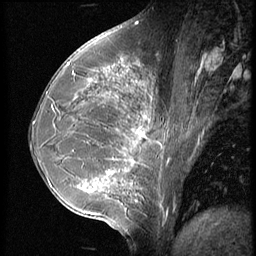
Breast MRI (dynamic contrast-enhanced), one sagittal slice. Position 26 of 56 along the scan axis. 3 images stored at this slice position (order not interpretable as contrast timing). 1.5 T. TE 4.2 ms, TR 9 ms. 2.5 mm slice thickness. 256 × 256 image matrix. Female patient, age 35 years. From the clinical record (not read from this slice): setting: breast cancer imaged before/during neoadjuvant chemotherapy; receptor status: HR-positive, HER2-negative.
Structures marked on this image (semi-automatically segmented with operator editing):
- analysis volume of interest (the breast-tissue region the enhancement analysis was run in; not a lesion): bounding box [x1, y1, x2, y2] px = [63, 60, 184, 218]
- tumour enhancement mask (voxels above the 140 % enhancement threshold inside the analysis volume of interest): [68, 64, 151, 192]